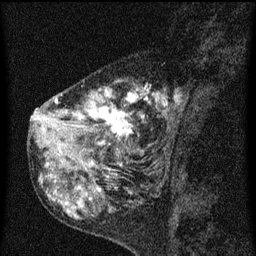
Breast MRI (dynamic contrast-enhanced), one sagittal slice. Slice 24 of 60 in the series (ordered by position). Dynamic contrast-enhanced series, image 2 of 3 at this slice position (ordered by acquisition). 1.5 T. TE 4.2 ms, TR 8 ms. 256 × 256 image matrix. Patient: female, 55 years.
Annotated regions visible in this slice (semi-automatic segmentation, software-assisted and operator-edited):
- analysis volume of interest (the breast-tissue region the enhancement analysis was run in; not a lesion): bounding box (x1, y1, x2, y2) in pixels: (42, 72, 185, 155)
- tumour enhancement mask (voxels above the 70 % enhancement threshold inside the analysis volume of interest): (55, 88, 181, 145)